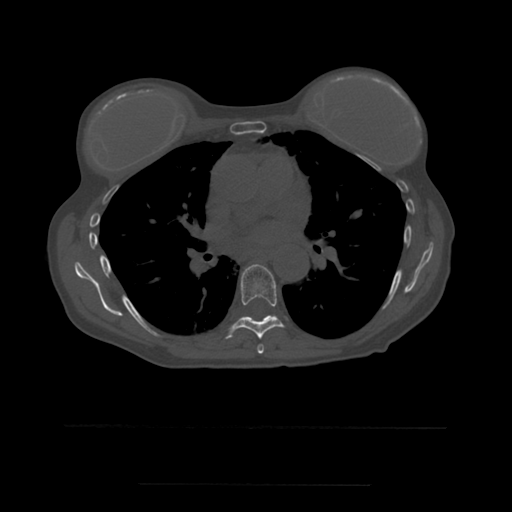
CT including the spine, one axial slice; position 358 of 544 along the scan axis; bone window (W 1800 / L 400 HU); 1.25 mm slice thickness; 512 × 512 image matrix, field of view 350 × 350 mm. Patient age 58 years. Case-level facts recorded for this patient, not image findings: primary cancer: lung.
Annotated regions visible in this slice (semi-automatic segmentation, software-assisted and operator-edited):
- T6 vertebra: bounding box (x1, y1, x2, y2) in pixels: (258, 344, 264, 354)
- T7 vertebra: (226, 264, 284, 339)